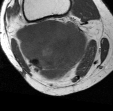
MRI of an extremity soft-tissue mass, one axial slice; slice 29 of 45 in the series (ordered by position); MR volume resampled by the dataset authors to the PET/CT grid (not the native acquisition matrix); 113 × 111 image matrix. Female patient. Case-level facts recorded for this patient, not image findings: histological type: liposarcoma; site of the primary tumour: right thigh.
Outlined on this slice (expert contour drawn on MRI and transferred to this co-registered scan by the dataset authors):
- gross tumour volume (mass): box from (x=17, y=19) to (x=91, y=82) px